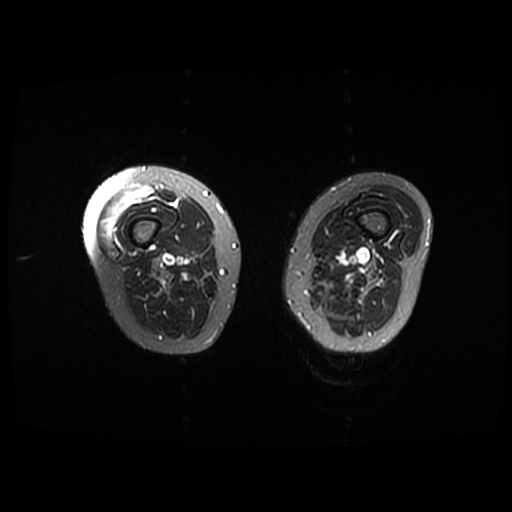
MRI of an extremity soft-tissue mass, one axial slice. Position 3 of 42 along the scan axis. T2-weighted fat-saturated. 512 × 512 image matrix. Female patient. Case-level facts recorded for this patient, not image findings: histological type: pleiomorphic undifferentiated sarcoma; grade: high; site of the primary tumour: right quadricep.
Annotated regions visible in this slice (manually delineated by an expert):
- gross tumour volume including surrounding oedema: box from (x=102, y=183) to (x=155, y=243) px